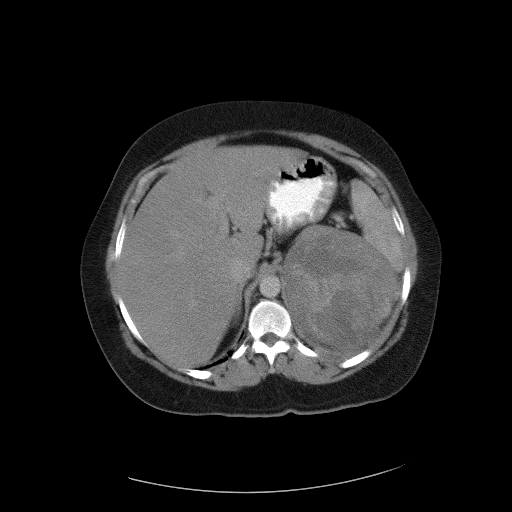
Contrast-enhanced abdominal CT, one axial slice. Slice 74 of 90 in the series (ordered by position). Reconstruction kernel FC01. Intravenous contrast given. Soft-tissue window (W 400 / L 40 HU). 5 mm slice thickness. 512 × 512 image matrix, field of view 480 × 480 mm. Patient: female, 55 years. From the clinical record (not read from this slice): diagnosis: adrenocortical carcinoma; tumour side: left adrenal; tumour size at pathology: 22 cm.
Outlined on this slice (semi-automatic segmentation, software-assisted and operator-edited):
- mass: box from (x=286, y=227) to (x=396, y=348) px